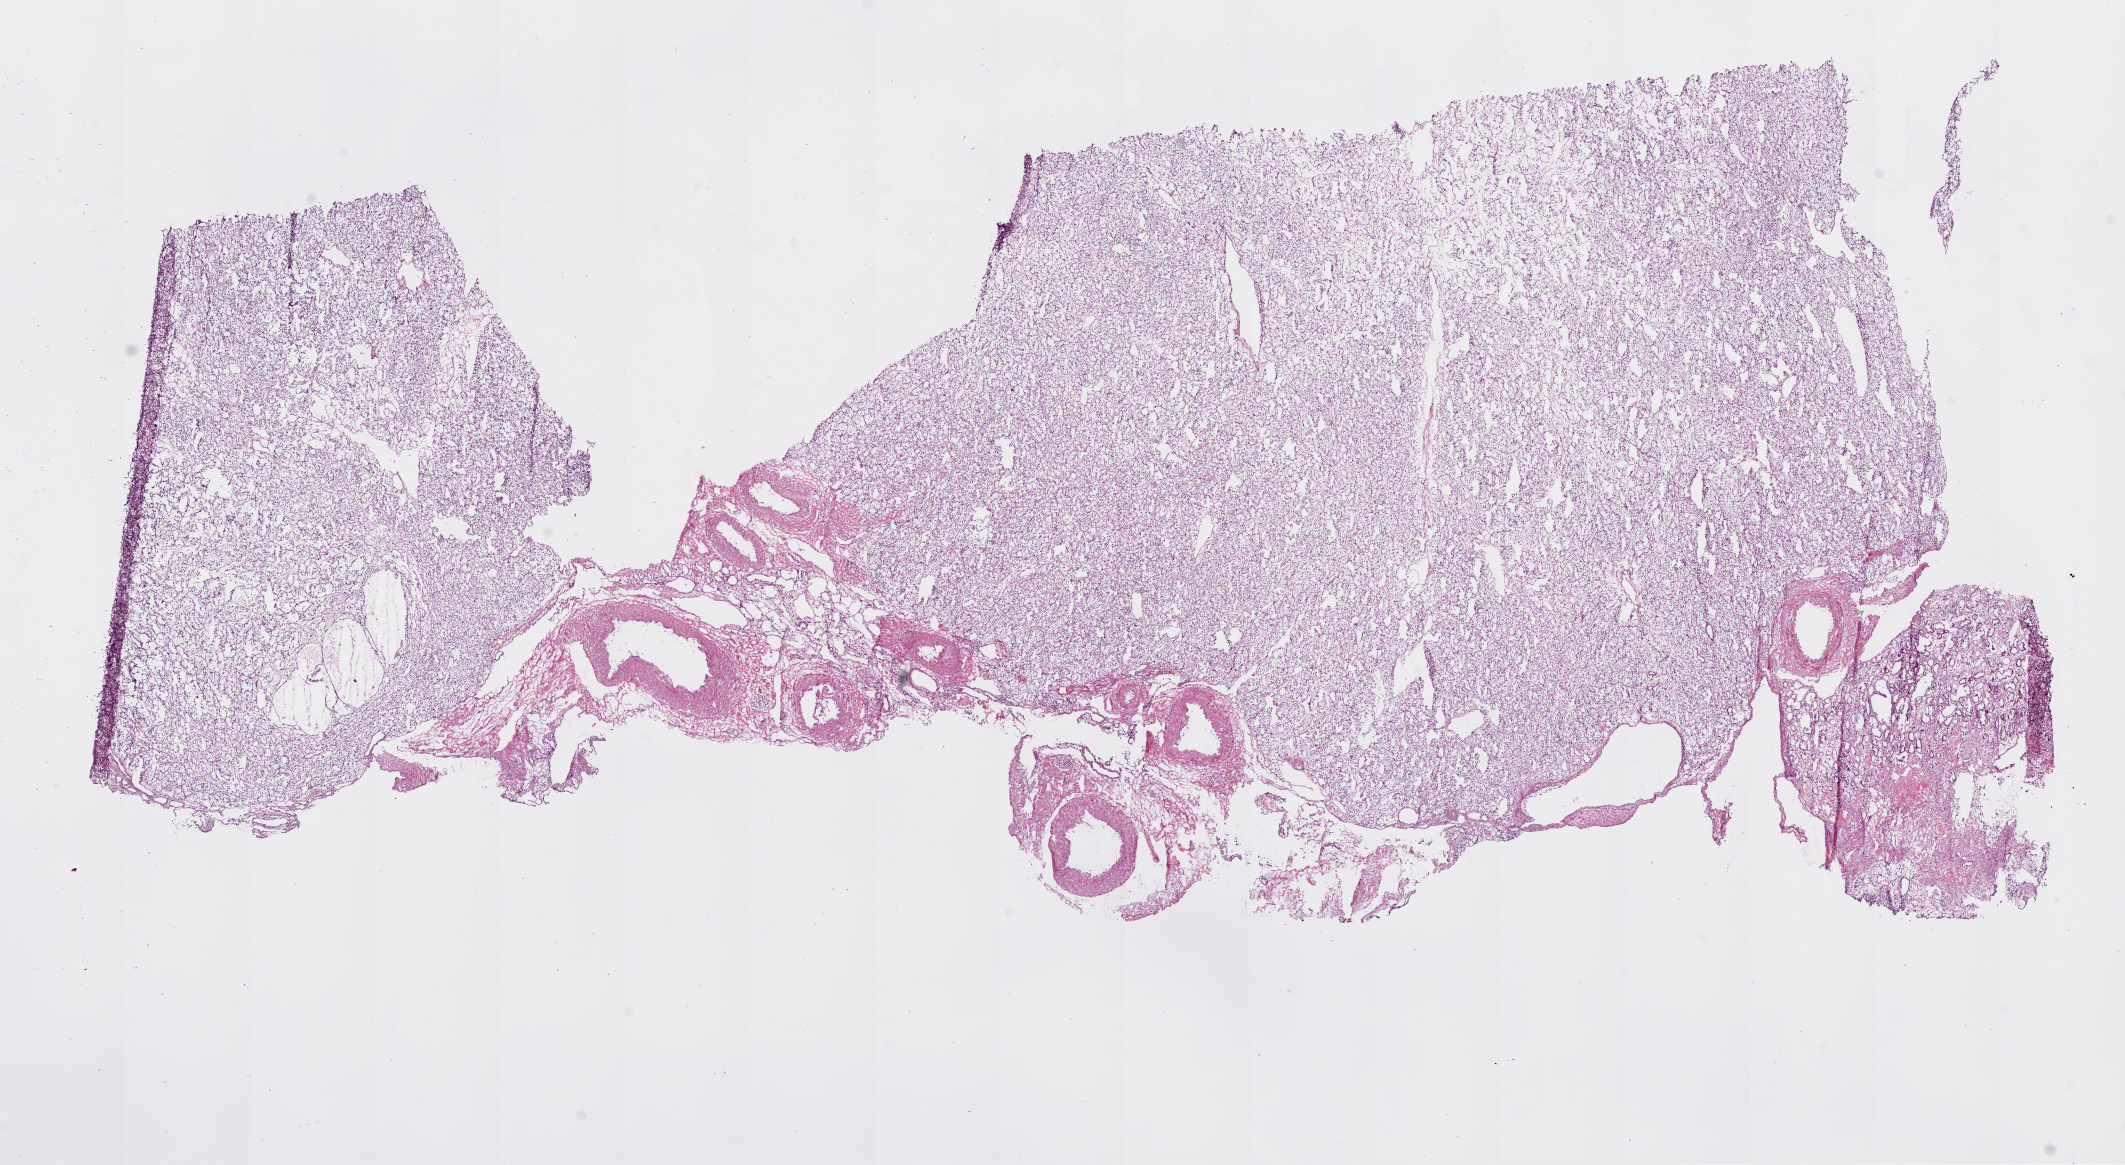
Whole-slide histology image, H&E, a low-resolution overview of the entire scanned area, about 17.1 x 9.3 mm. Frozen section. Primary tumour sample from the kidney. Female patient; age at initial diagnosis 51 years.
Histologic diagnosis: Clear cell adenocarcinoma, NOS.